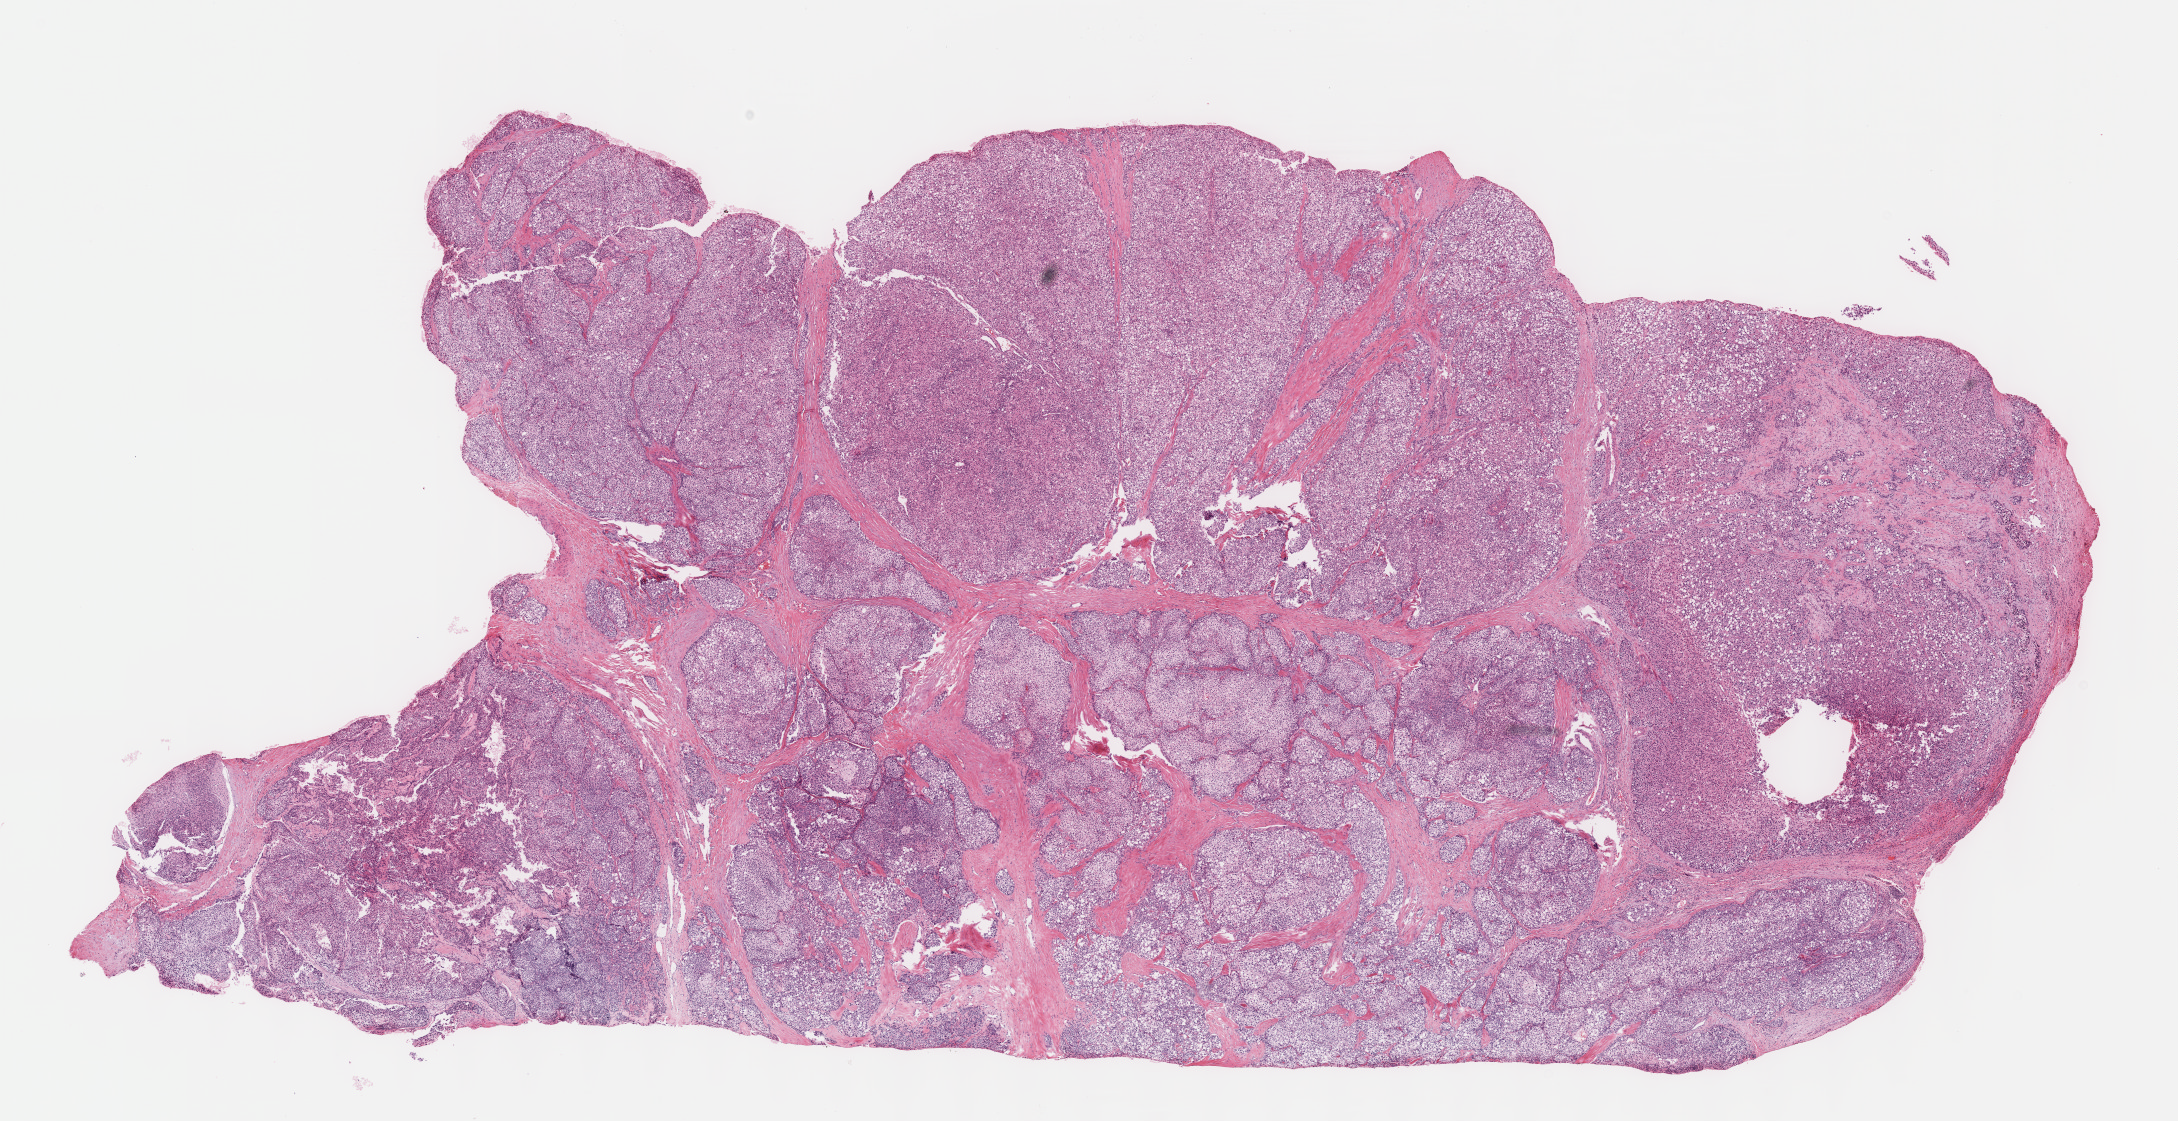
Digitized H&E-stained tissue section (whole slide), low-resolution overview of the scanned area, about 17.6 x 9.1 mm, formalin-fixed paraffin-embedded (FFPE) diagnostic section, liver, primary tumour sample. Male, age 48 years at initial diagnosis. Histologic grade: G3 (poorly differentiated).
Pathologic diagnosis: Hepatocellular carcinoma, NOS. AJCC pathologic stage: I (7th edition).